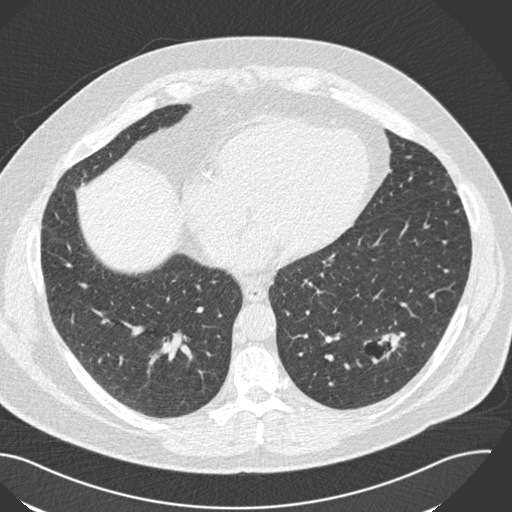
Low-dose screening chest CT, one axial slice; position 66 of 153 along the scan axis; reconstruction kernel B30f; 120 kVp; lung window (W 1500 / L -600 HU); 2 mm slice thickness; 512 × 512 image matrix.
Outlined on this slice (expert manual segmentation):
- lesion 1 (tumor, lower lobe of left lung): bounding box [x1, y1, x2, y2] px = [378, 333, 405, 353]